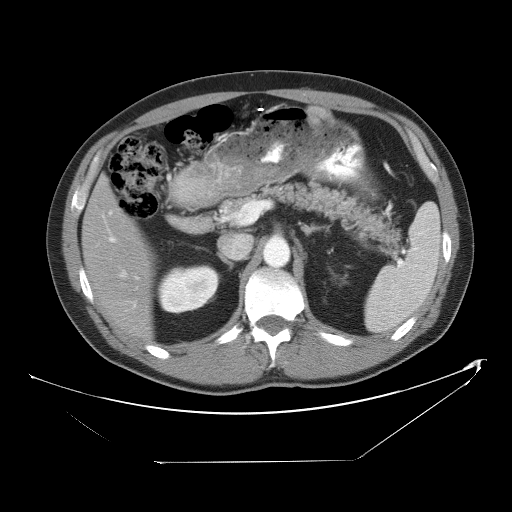
Contrast-enhanced abdominal CT, one axial slice; slice 28 of 53 in the series (ordered by position); reconstruction kernel STANDARD; 120 kVp; intravenous contrast given; soft-tissue window (W 400 / L 40 HU); 512 × 512 image matrix, field of view 438 × 438 mm. Male patient, age 59 years. Case-level facts recorded for this patient, not image findings: diagnosis: colorectal cancer liver metastases, imaged before liver resection; multiple liver metastases: yes; largest metastasis: 8.5 cm.
Structures marked on this image (expert manual segmentation):
- hepatic veins: box from (x=109, y=211) to (x=126, y=277) px
- liver: (x=83, y=181)–(x=152, y=339)
- planned liver remnant (the part of the liver to remain after resection): (x=83, y=181)–(x=151, y=340)
- portal vein (with intrahepatic branches): (x=110, y=237)–(x=138, y=303)